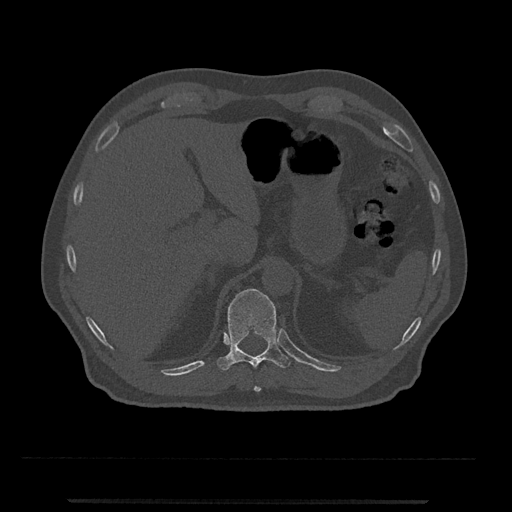
CT including the spine, one axial slice; position 469 of 797 along the scan axis; reconstruction kernel Br40s/3; 120 kVp; bone window (W 1800 / L 400 HU); 0.5 mm slice thickness; 512 × 512 image matrix, field of view 419 × 419 mm. Male patient, age 63 years. Case-level facts recorded for this patient, not image findings: primary cancer: prostate.
Annotated regions visible in this slice (semi-automatically segmented with operator editing):
- T10 vertebra: bounding box <254,386,261,392> (left, top, right, bottom; pixels)
- T11 vertebra: <217,289,290,371>